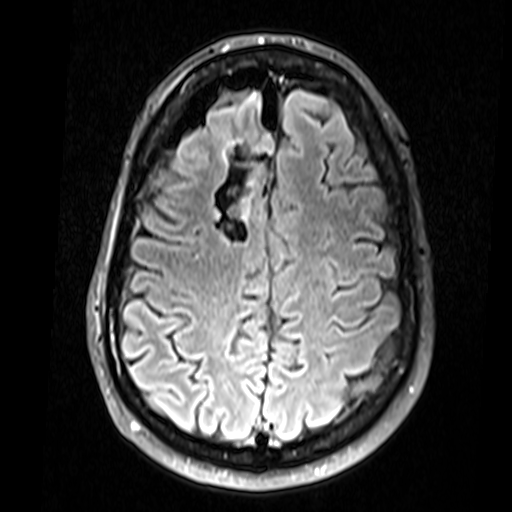
Brain MRI from a brain-tumour surgery series, one axial slice; slice 47 of 74 in the series (ordered by position); T2 FLAIR; 512 × 512 image matrix. Case-level facts recorded for this patient, not image findings: histopathology: Glial fibroma; tumour location: Right Frontal.
Structures marked on this image (manually delineated by an expert):
- residual tumour: bounding box (x1, y1, x2, y2) in pixels: (237, 198, 251, 223)